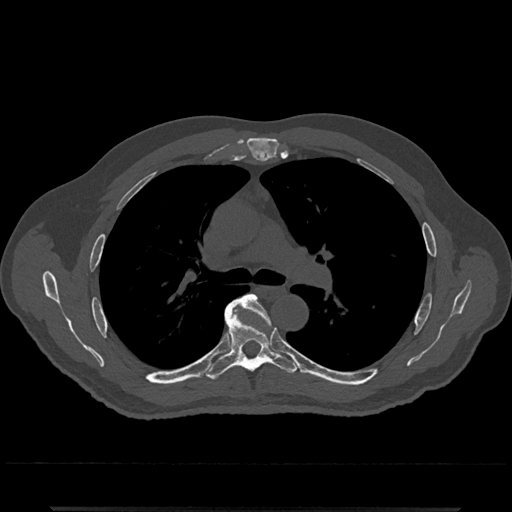
CT including the spine, one axial slice; position 788 of 797 along the scan axis; reconstruction kernel Br40s/3; 120 kVp; bone window (W 1800 / L 400 HU); 0.5 mm slice thickness; 512 × 512 image matrix, field of view 393 × 393 mm. Male patient, age 67 years. From the clinical record (not read from this slice): primary cancer: prostate.
Outlined on this slice (semi-automatic segmentation, software-assisted and operator-edited):
- T5 vertebra: bounding box [x1, y1, x2, y2] px = [233, 294, 269, 319]
- T6 vertebra: [204, 301, 298, 380]